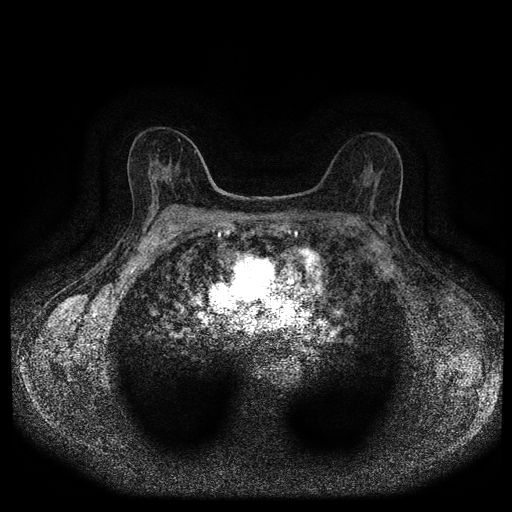
Breast MRI (dynamic contrast-enhanced, multi-phase), one axial slice. Slice 57 of 116 in the series (ordered by position). Dynamic contrast-enhanced series, time point 2 of 5 at this slice position (early post-contrast). 1.5 T. TE 2.7 ms, TR 5.4 ms. 2 mm slice thickness. 512 × 512 image matrix, field of view 330 × 330 mm. Patient: female, 63 years.
Outlined on this slice (semi-automatic segmentation, software-assisted and operator-edited):
- breast lesion (labelled 'tumour' in the annotation; benign lesions carry a separate 'benign' label): bounding box (x1, y1, x2, y2) in pixels: (378, 223, 390, 240)